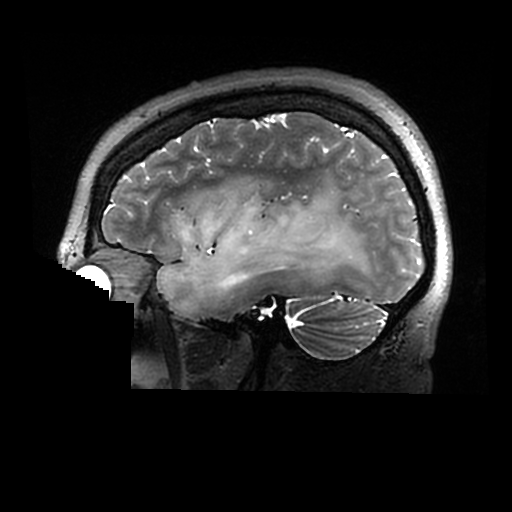
Brain MRI from a brain-tumour surgery series, one sagittal slice; position 216 of 320 along the scan axis; 512 × 512 image matrix. From the clinical record (not read from this slice): histopathology: Astrocytoma; WHO grade: 2; IDH mutation: yes.
Structures marked on this image (manually delineated by an expert):
- tumour: bounding box [x1, y1, x2, y2] px = [157, 185, 379, 312]